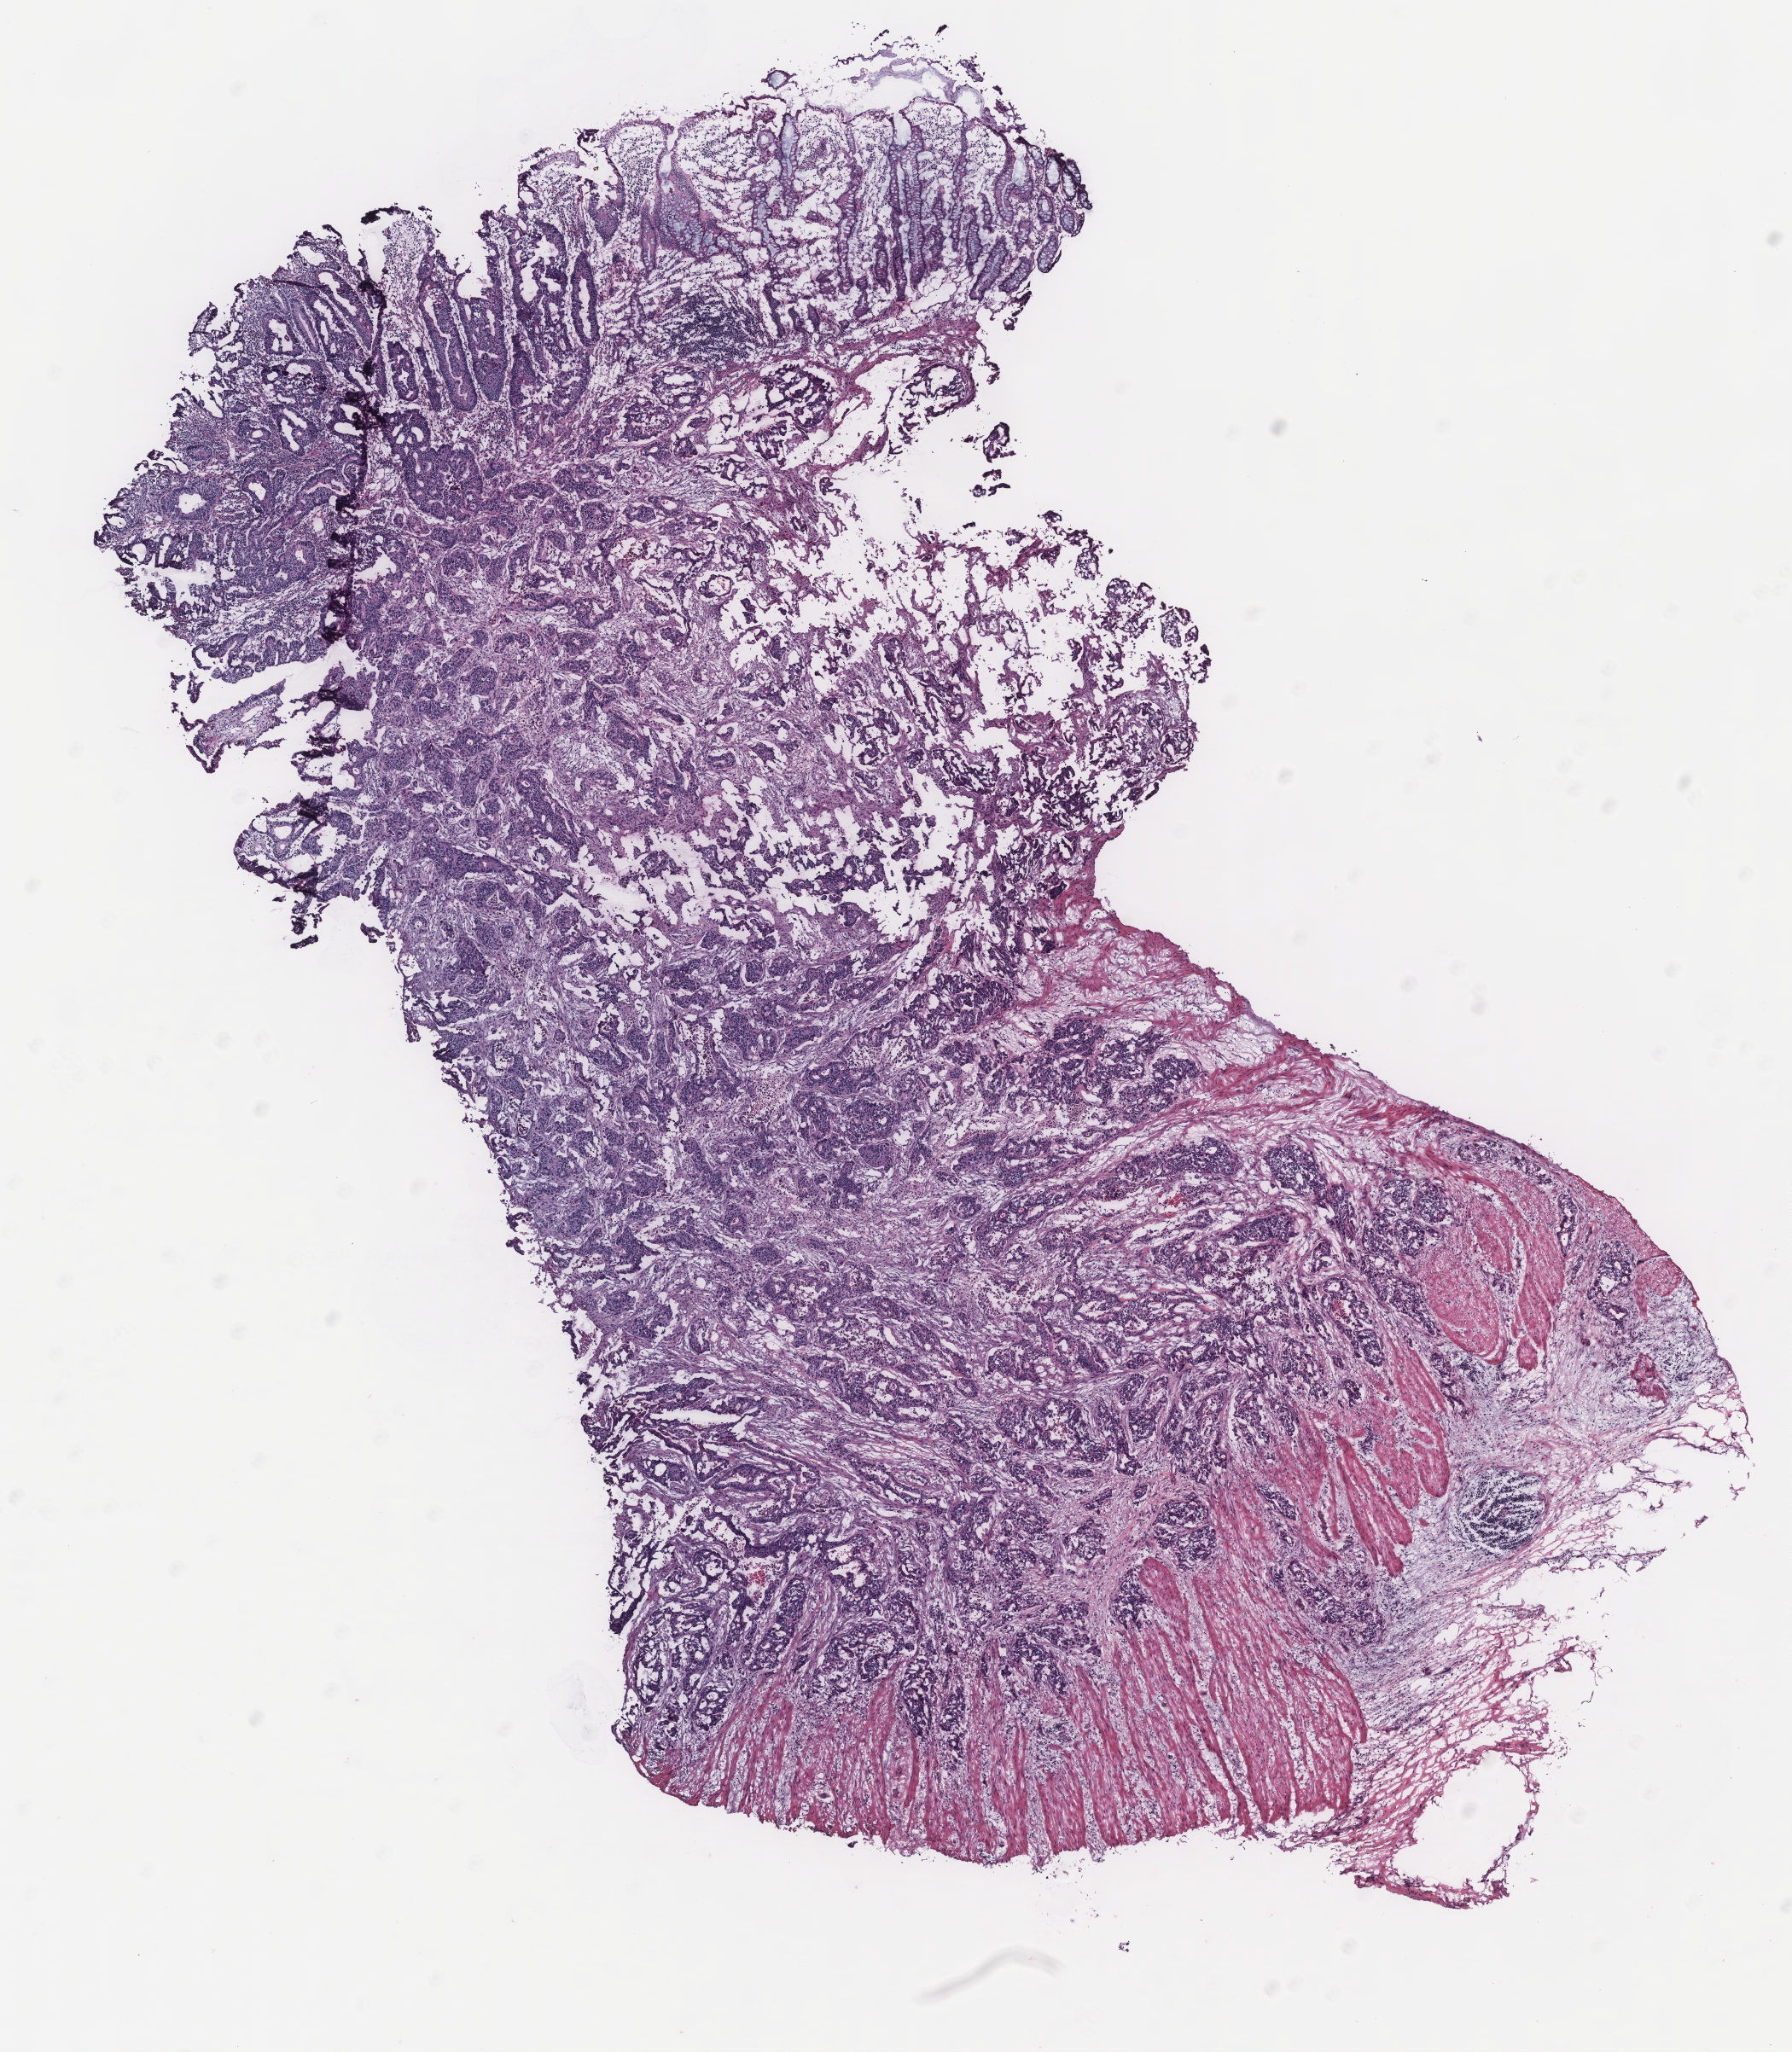
Whole-slide histology image, Hematoxylin and eosin (H&E) stained, low-resolution overview of the scanned area, about 8.4 x 9.6 mm (acquisition: 40x scan); colon, normal (non-tumour) tissue. 73-year-old female patient.
- this section: normal (non-tumour) tissue from the same patient
- patient diagnosis: Adenocarcinoma, NOS